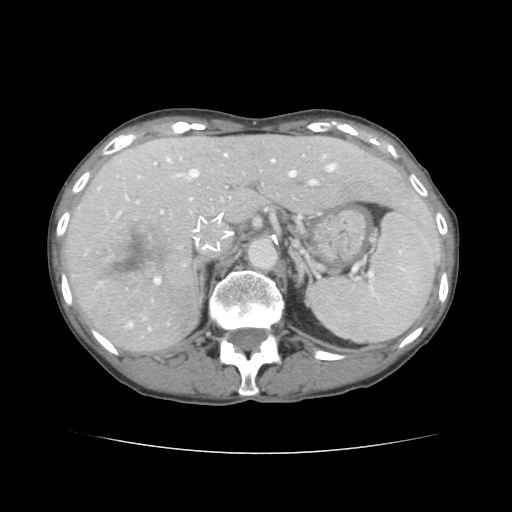
Contrast-enhanced abdominal CT, one axial slice. Slice 96 of 136 in the series (ordered by position). 120 kVp. Intravenous contrast given. Soft-tissue window (W 400 / L 40 HU). 512 × 512 image matrix, field of view 319 × 319 mm. Female patient, age 77 years. From the clinical record (not read from this slice): diagnosis: colorectal cancer liver metastases, imaged before liver resection; multiple liver metastases: yes; largest metastasis: 3 cm; chemotherapy before resection: yes.
Structures marked on this image (outlined manually by an expert reader):
- hepatic veins: box from (x=128, y=154) to (x=335, y=330) px
- liver: (x=66, y=136)–(x=438, y=353)
- planned liver remnant (the part of the liver to remain after resection): (x=155, y=136)–(x=437, y=243)
- portal vein (with intrahepatic branches): (x=117, y=163)–(x=320, y=284)
- liver metastasis: (x=83, y=218)–(x=175, y=290)